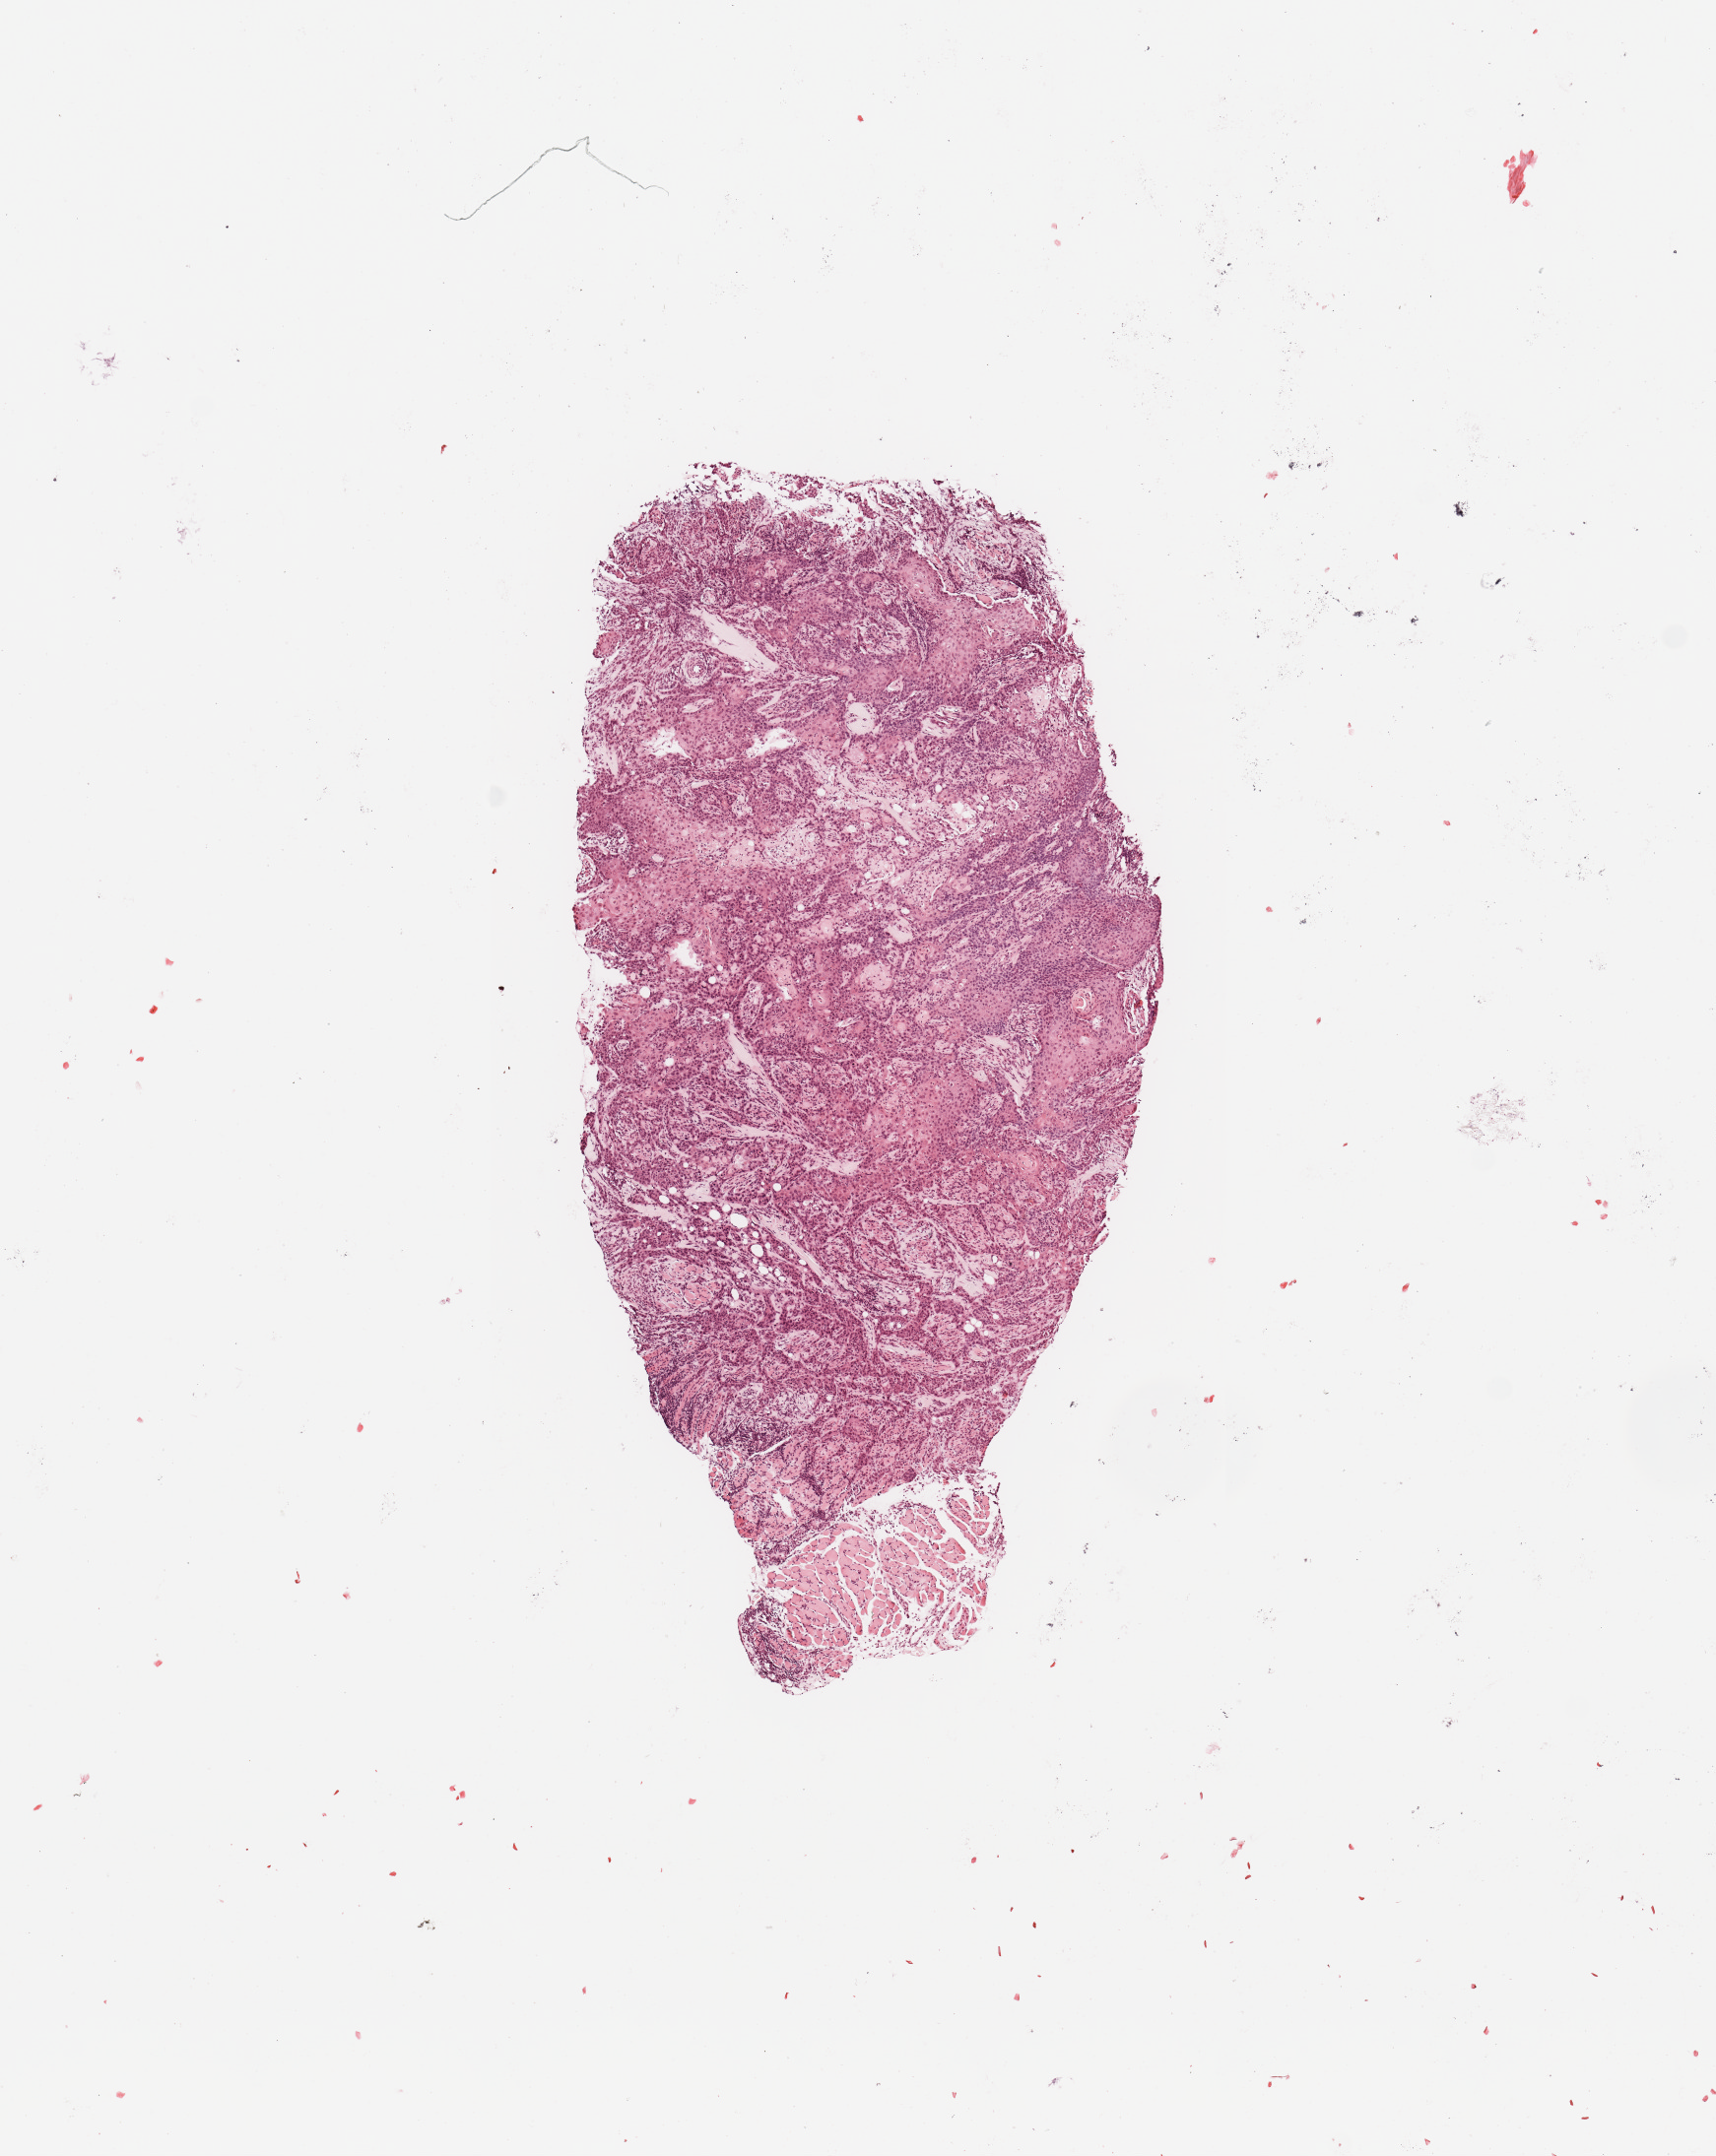
Whole-slide histology image, Hematoxylin and eosin (H&E) stained, low-resolution overview of the scanned area, about 6.9 x 8.7 mm, tumour tissue sample, sampled site: floor of mouth. 49-year-old male patient. Histologic grade: G2 (moderately differentiated). Composition of this section per pathologist review: tumour nuclei 85%, necrosis 5%.
* AJCC pathologic stage: IVA
* primary tumour site (as recorded): oral cavity
* diagnosis: Squamous cell carcinoma, NOS (floor of mouth, NOS)